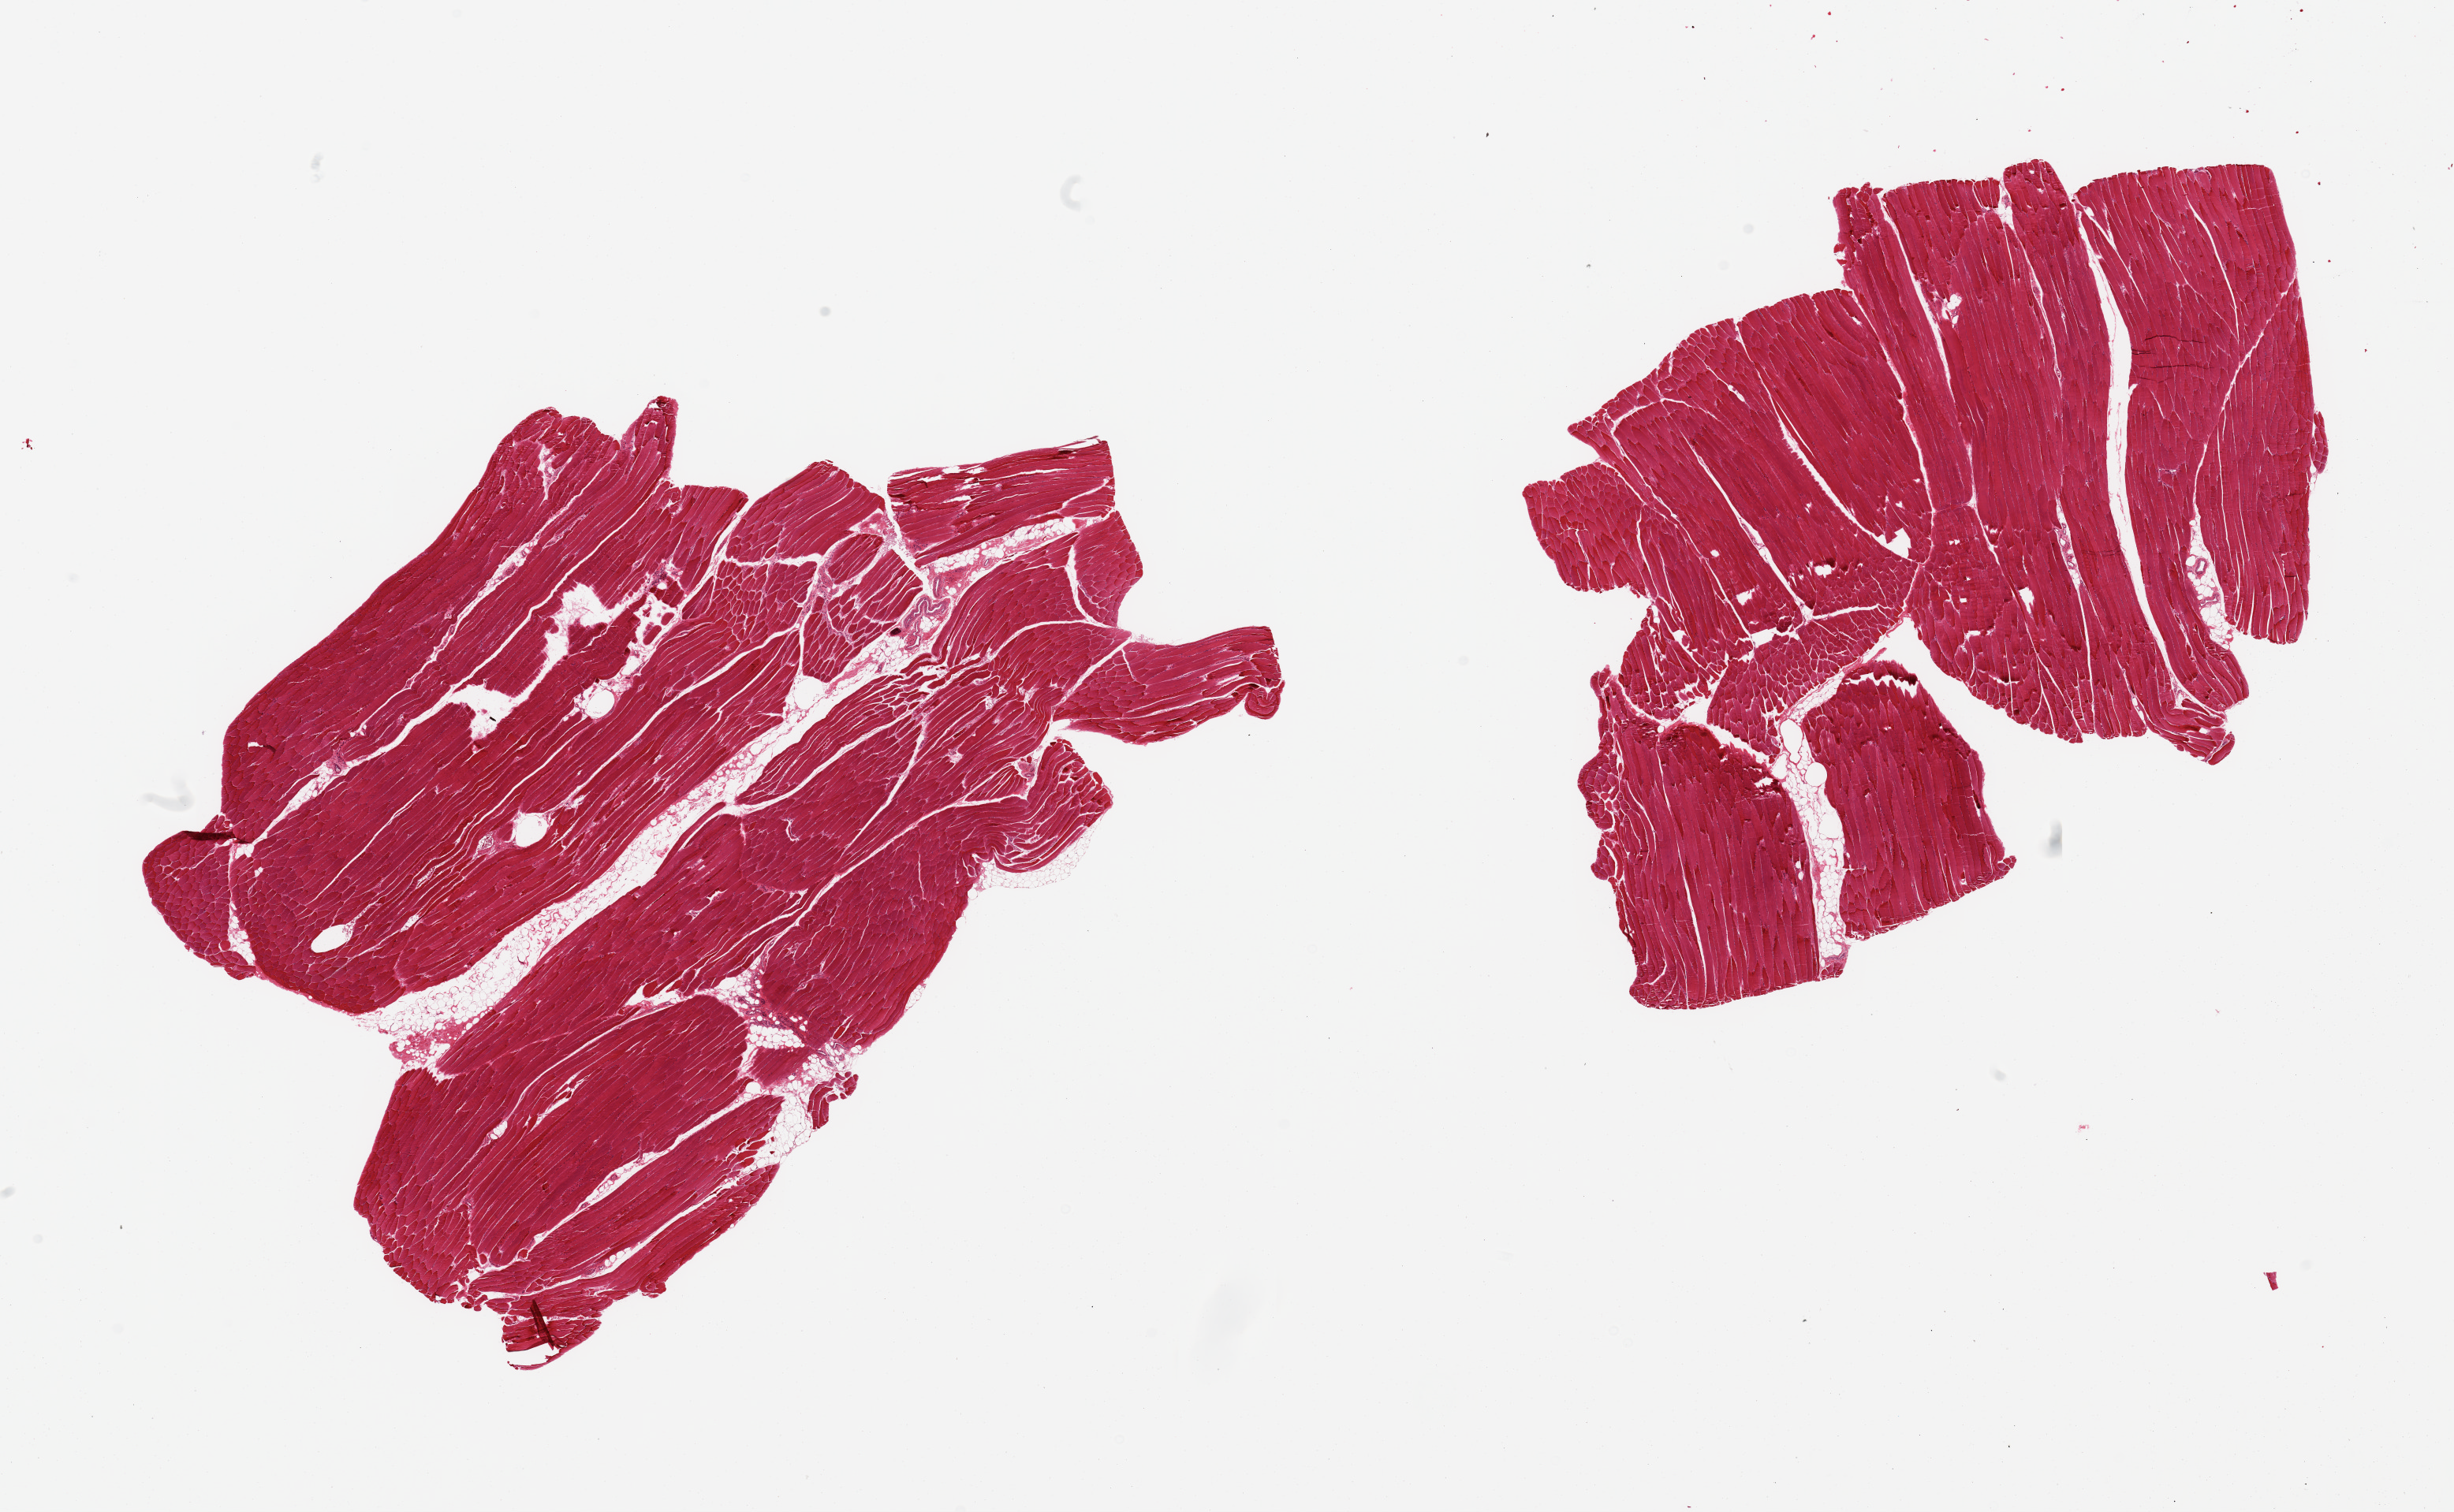
Whole-slide image, haematoxylin and eosin stain, brightfield — low-resolution overview of the scanned area, about 24.6 x 15.2 mm. PAXgene-fixed, paraffin-embedded tissue. Sampled site (target tissue): skeletal muscle. Tissue donor sample. Donor: male.
Pathologist's review note for this sample: 2 pieces; 5% internal fat.